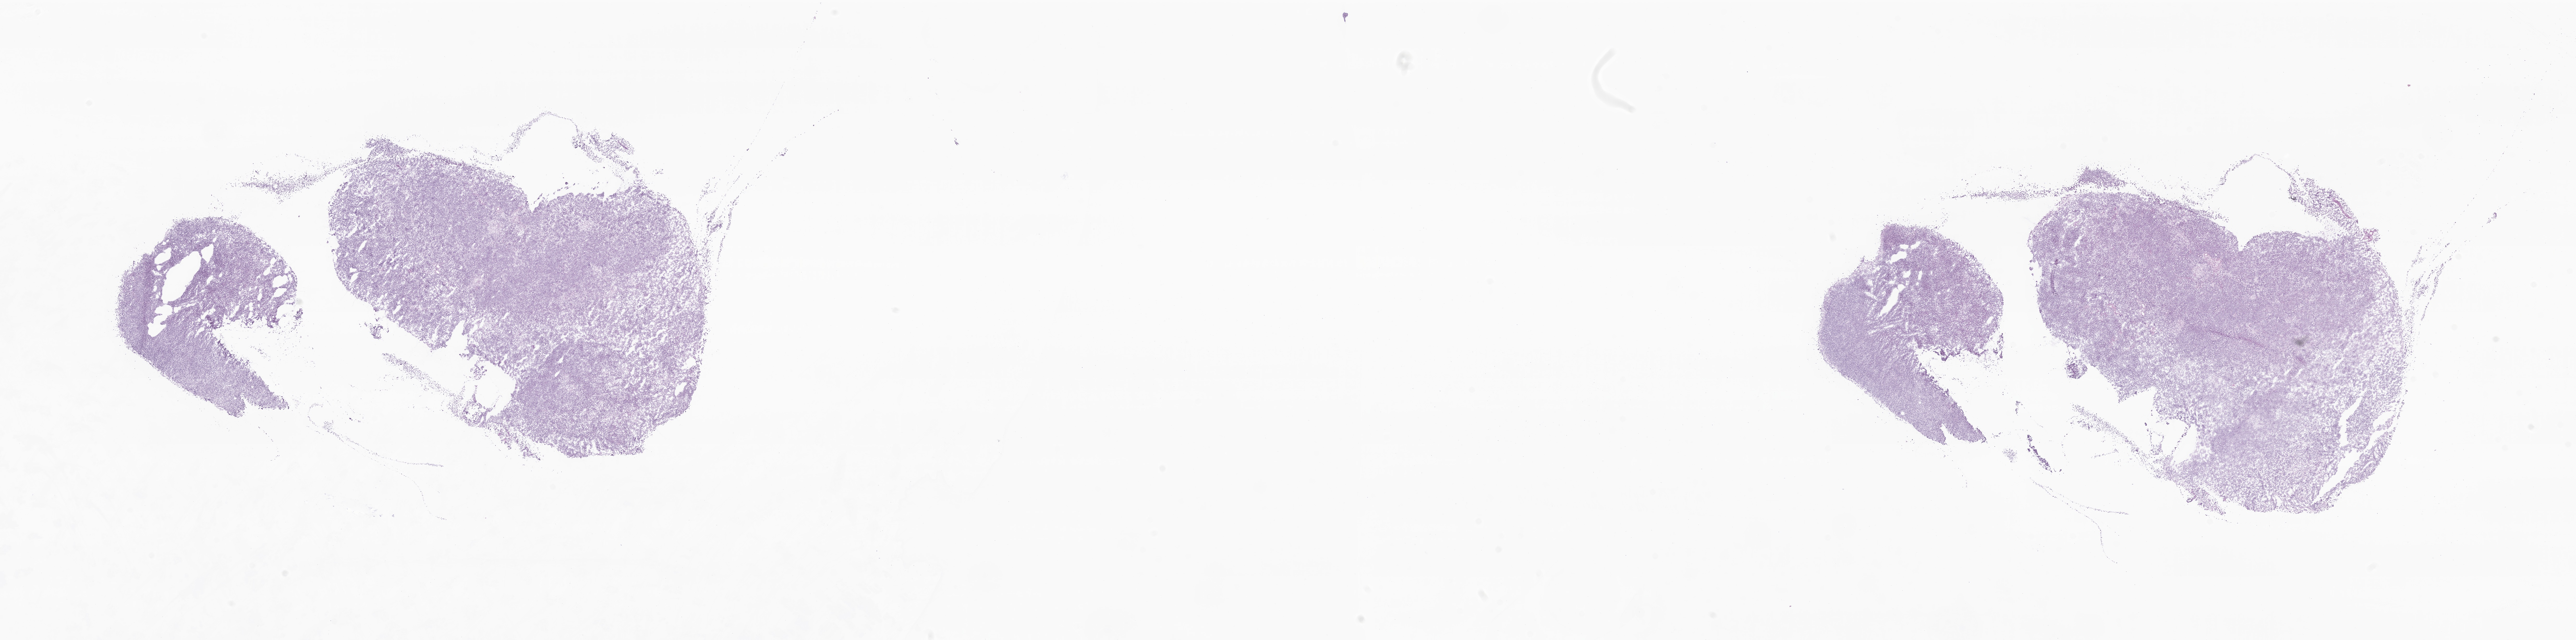
Digitized haematoxylin and eosin-stained section of tumor tissue from the brain, low-resolution overview of the scanned area, about 41.7 x 10.3 mm, frozen section. Patient: female, age 76 months (6 years 4 months).
Diagnosis: Medulloblastoma, NOS.